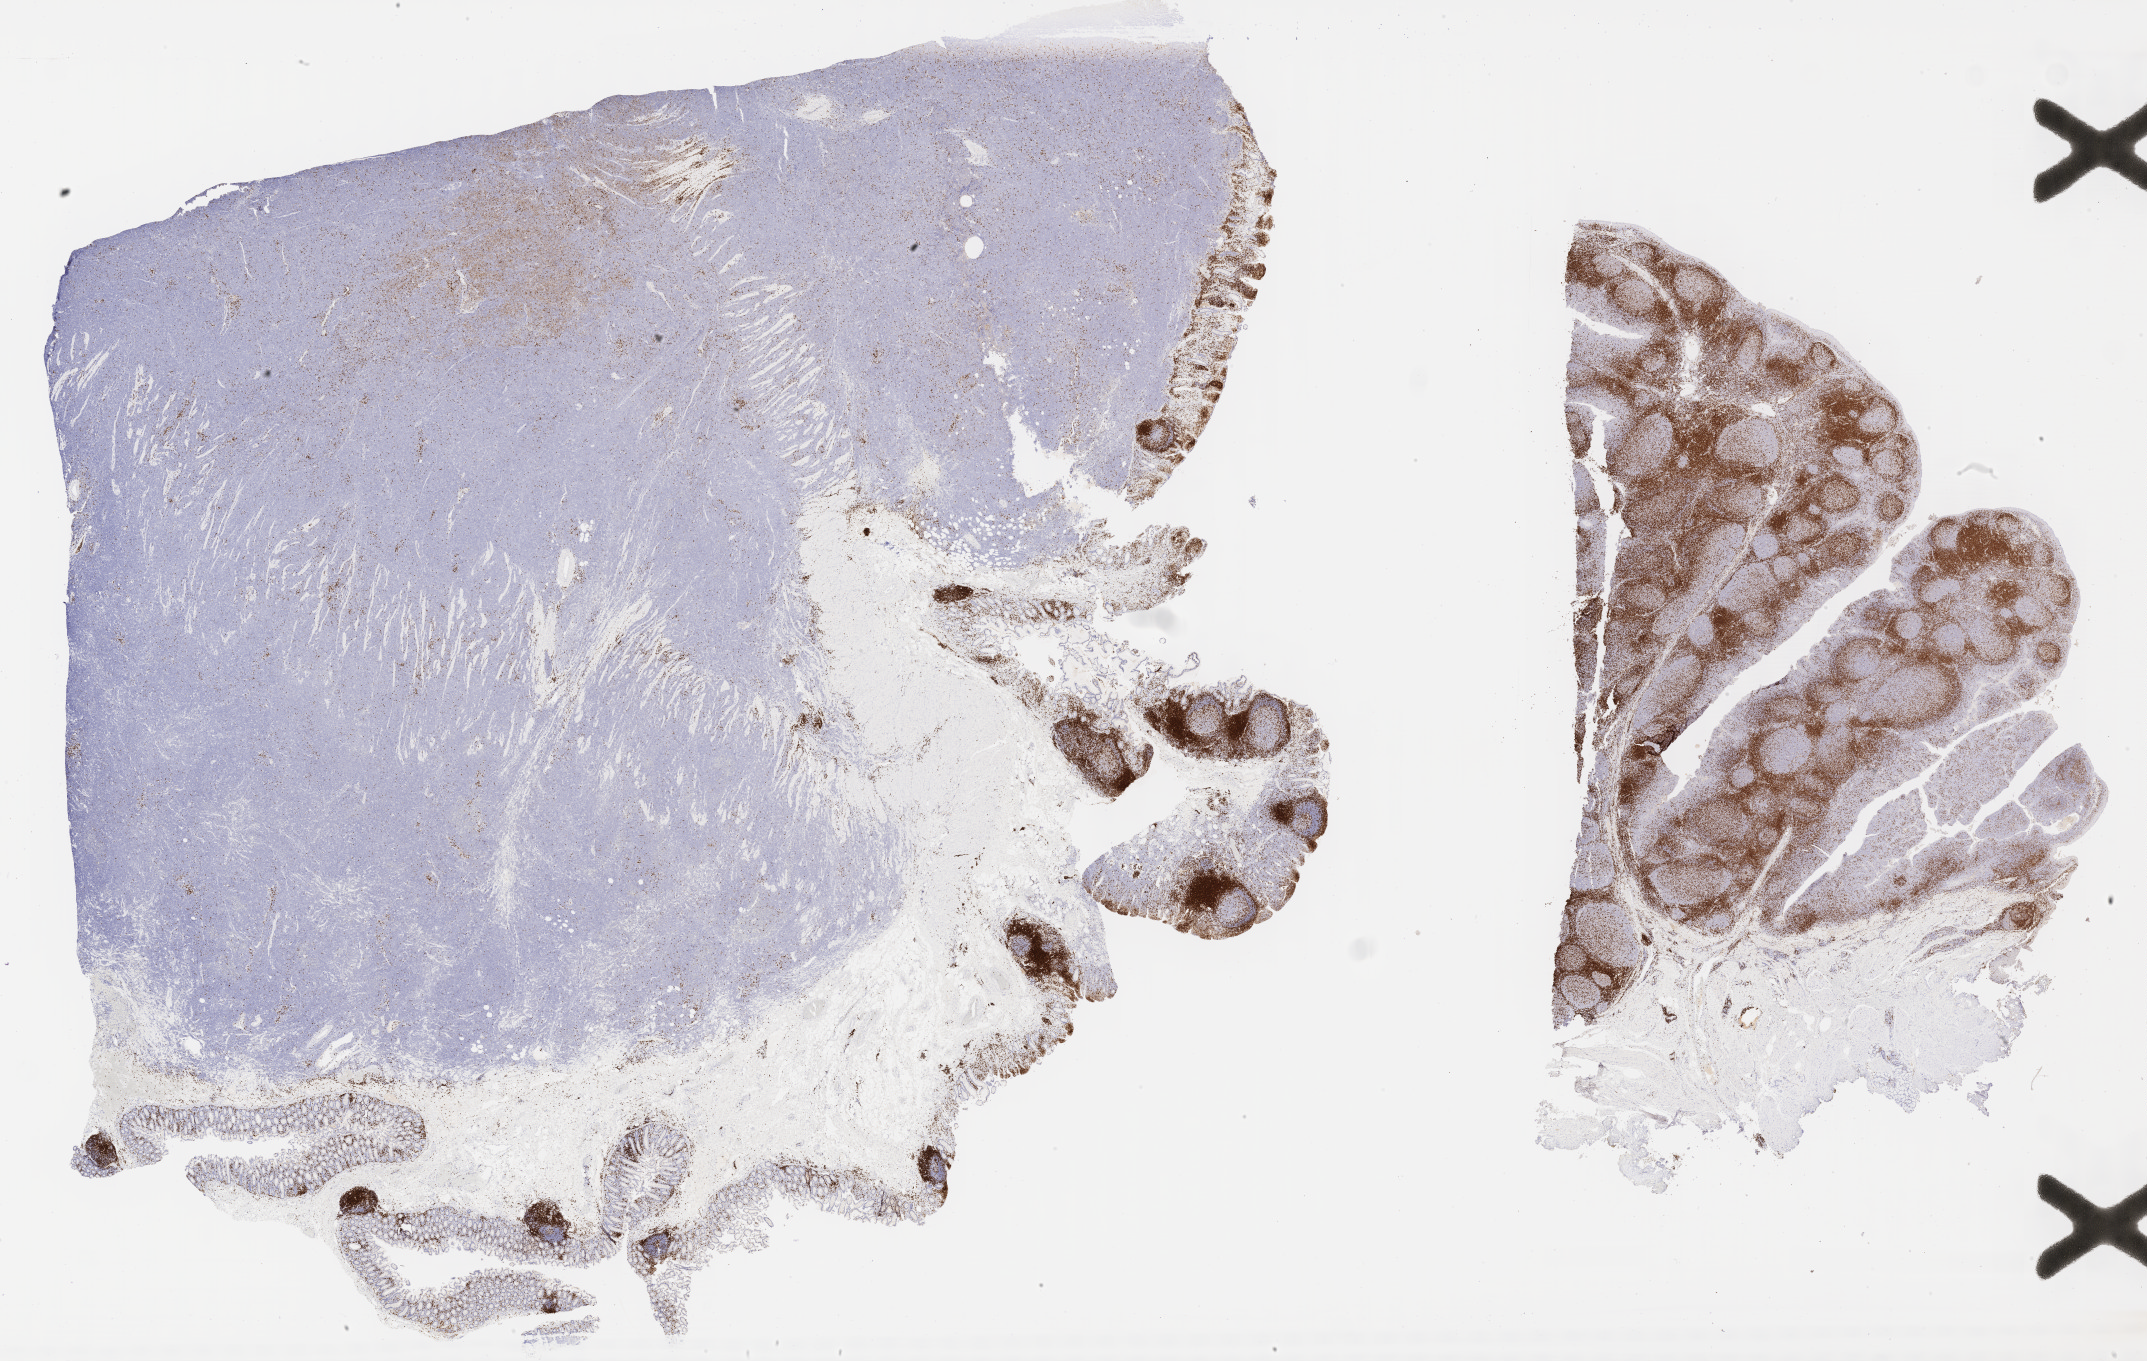
IHC for CD3, whole-slide image — low-resolution overview of the scanned area, about 34.7 x 22.0 mm. Specimen: tumor tissue. Male patient, 59 years old.
- histologic diagnosis: Burkitt lymphoma, NOS